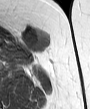
MRI of an extremity soft-tissue mass, one axial slice; slice 25 of 45 in the series (ordered by position); MR volume resampled by the dataset authors to the PET/CT grid (not the native acquisition matrix); 3.27 mm slice thickness; 90 × 109 image matrix. Female patient. Case-level facts recorded for this patient, not image findings: histological type: leiomyosarcoma; grade: intermediate; site of the primary tumour: parascapusular.
Outlined on this slice (expert contour drawn on MRI and transferred to this co-registered scan by the dataset authors):
- gross tumour volume including surrounding oedema: box from (x=19, y=27) to (x=50, y=58) px
- gross tumour volume (mass): (x=21, y=27)–(x=48, y=52)